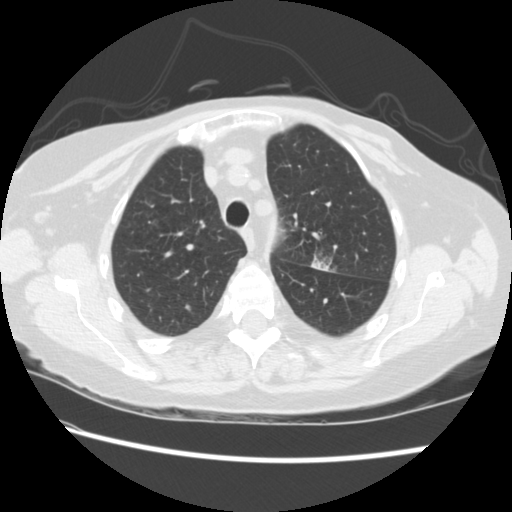
Low-dose screening chest CT, one axial slice; slice 166 of 224 in the series (ordered by position); reconstruction kernel STANDARD; lung window (W 1500 / L -600 HU); 2.5 mm slice thickness; 512 × 512 image matrix, field of view 340 × 340 mm.
Outlined on this slice (outlined manually by an expert reader):
- lesion 1 (tumor, upper lobe of left lung): bounding box [x1, y1, x2, y2] px = [312, 258, 330, 271]